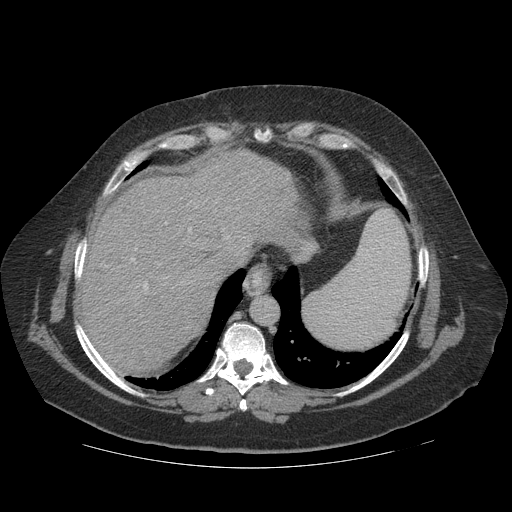
Contrast-enhanced abdominal CT (liver protocol), one axial slice; position 96 of 121 along the scan axis; reconstruction kernel STANDARD; 140 kVp; soft-tissue window (W 400 / L 40 HU); 512 × 512 image matrix, field of view 420 × 420 mm. Case-level facts recorded for this patient, not image findings: diagnosis: hepatocellular carcinoma (patient treated with transarterial chemoembolisation; whether this scan precedes or follows treatment is not stated here); TNM stage (as recorded): Stage-IIIA; Child-Pugh class: A; tumour differentiation: well differentiated; tumour nodularity: multinodular.
Annotated regions visible in this slice (semi-automatically segmented with operator editing):
- abdominal aorta: bounding box <251,297,278,325> (left, top, right, bottom; pixels)
- liver parenchyma outside the tumour (the mass and vessels are separate outlines, so this box may not span the whole liver): <80,150,318,372>
- liver vessels: <106,206,230,291>